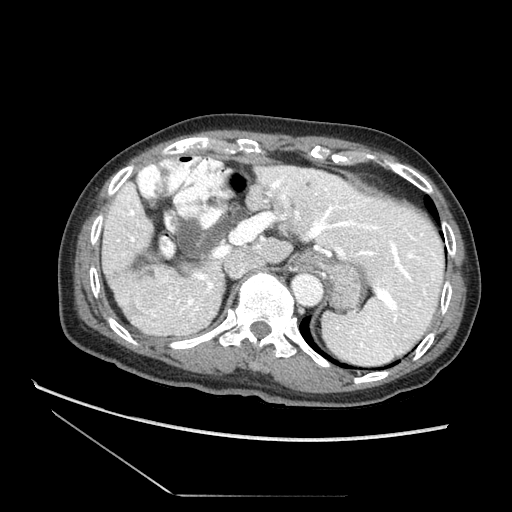
Contrast-enhanced abdominal CT (liver protocol), one axial slice; position 55 of 73 along the scan axis; reconstruction kernel STANDARD; 120 kVp; soft-tissue window (W 400 / L 40 HU); 2.5 mm slice thickness; 512 × 512 image matrix. Case-level facts recorded for this patient, not image findings: diagnosis: hepatocellular carcinoma (patient treated with transarterial chemoembolisation; whether this scan precedes or follows treatment is not stated here); TNM stage (as recorded): Stage-II; Child-Pugh class: A; tumour differentiation: moderately differentiated; tumour size: 3.8 cm.
Structures marked on this image (semi-automatically segmented with operator editing):
- liver parenchyma outside the tumour (the mass and vessels are separate outlines, so this box may not span the whole liver): box from (x=104, y=165) to (x=446, y=355) px
- mass: (x=139, y=279)–(x=178, y=313)
- liver vessels: (x=161, y=229)–(x=410, y=312)